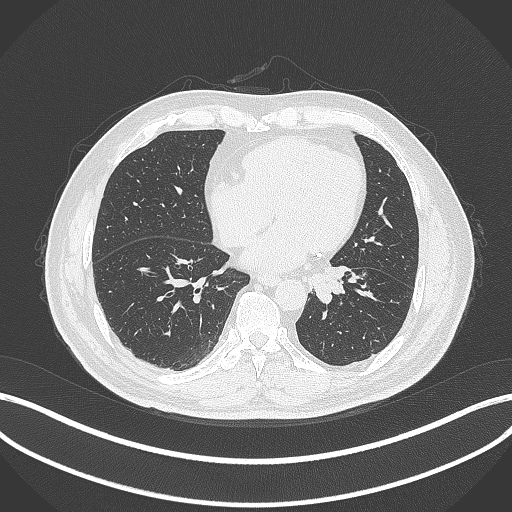
Chest CT, one axial slice; position 96 of 312 along the scan axis; 120 kVp; lung window (W 1500 / L -600 HU); 1 mm slice thickness; 512 × 512 image matrix, field of view 400 × 400 mm. Male patient, age 71 years. From the clinical record (not read from this slice): clinical TNM (as recorded): T1b N0 M0.
Outlined on this slice (rectangle marked by the reading radiologist):
- lung tumour (recorded histology: squamous cell carcinoma): bounding box (x1, y1, x2, y2) in pixels: (306, 262, 351, 304)